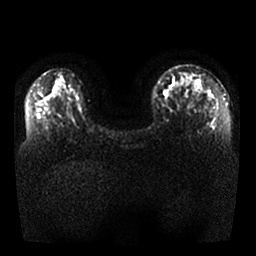
Breast MRI, one axial slice. Position 14 of 25 along the scan axis. Diffusion-weighted series; image 2 of 4 stored at this slice position (different b-values; order by instance number). 1.5 T. 4 mm slice thickness. 256 × 256 image matrix. Female patient.
Structures marked on this image (expert manual segmentation):
- tumour on diffusion-weighted imaging: bounding box [x1, y1, x2, y2] px = [183, 71, 215, 99]